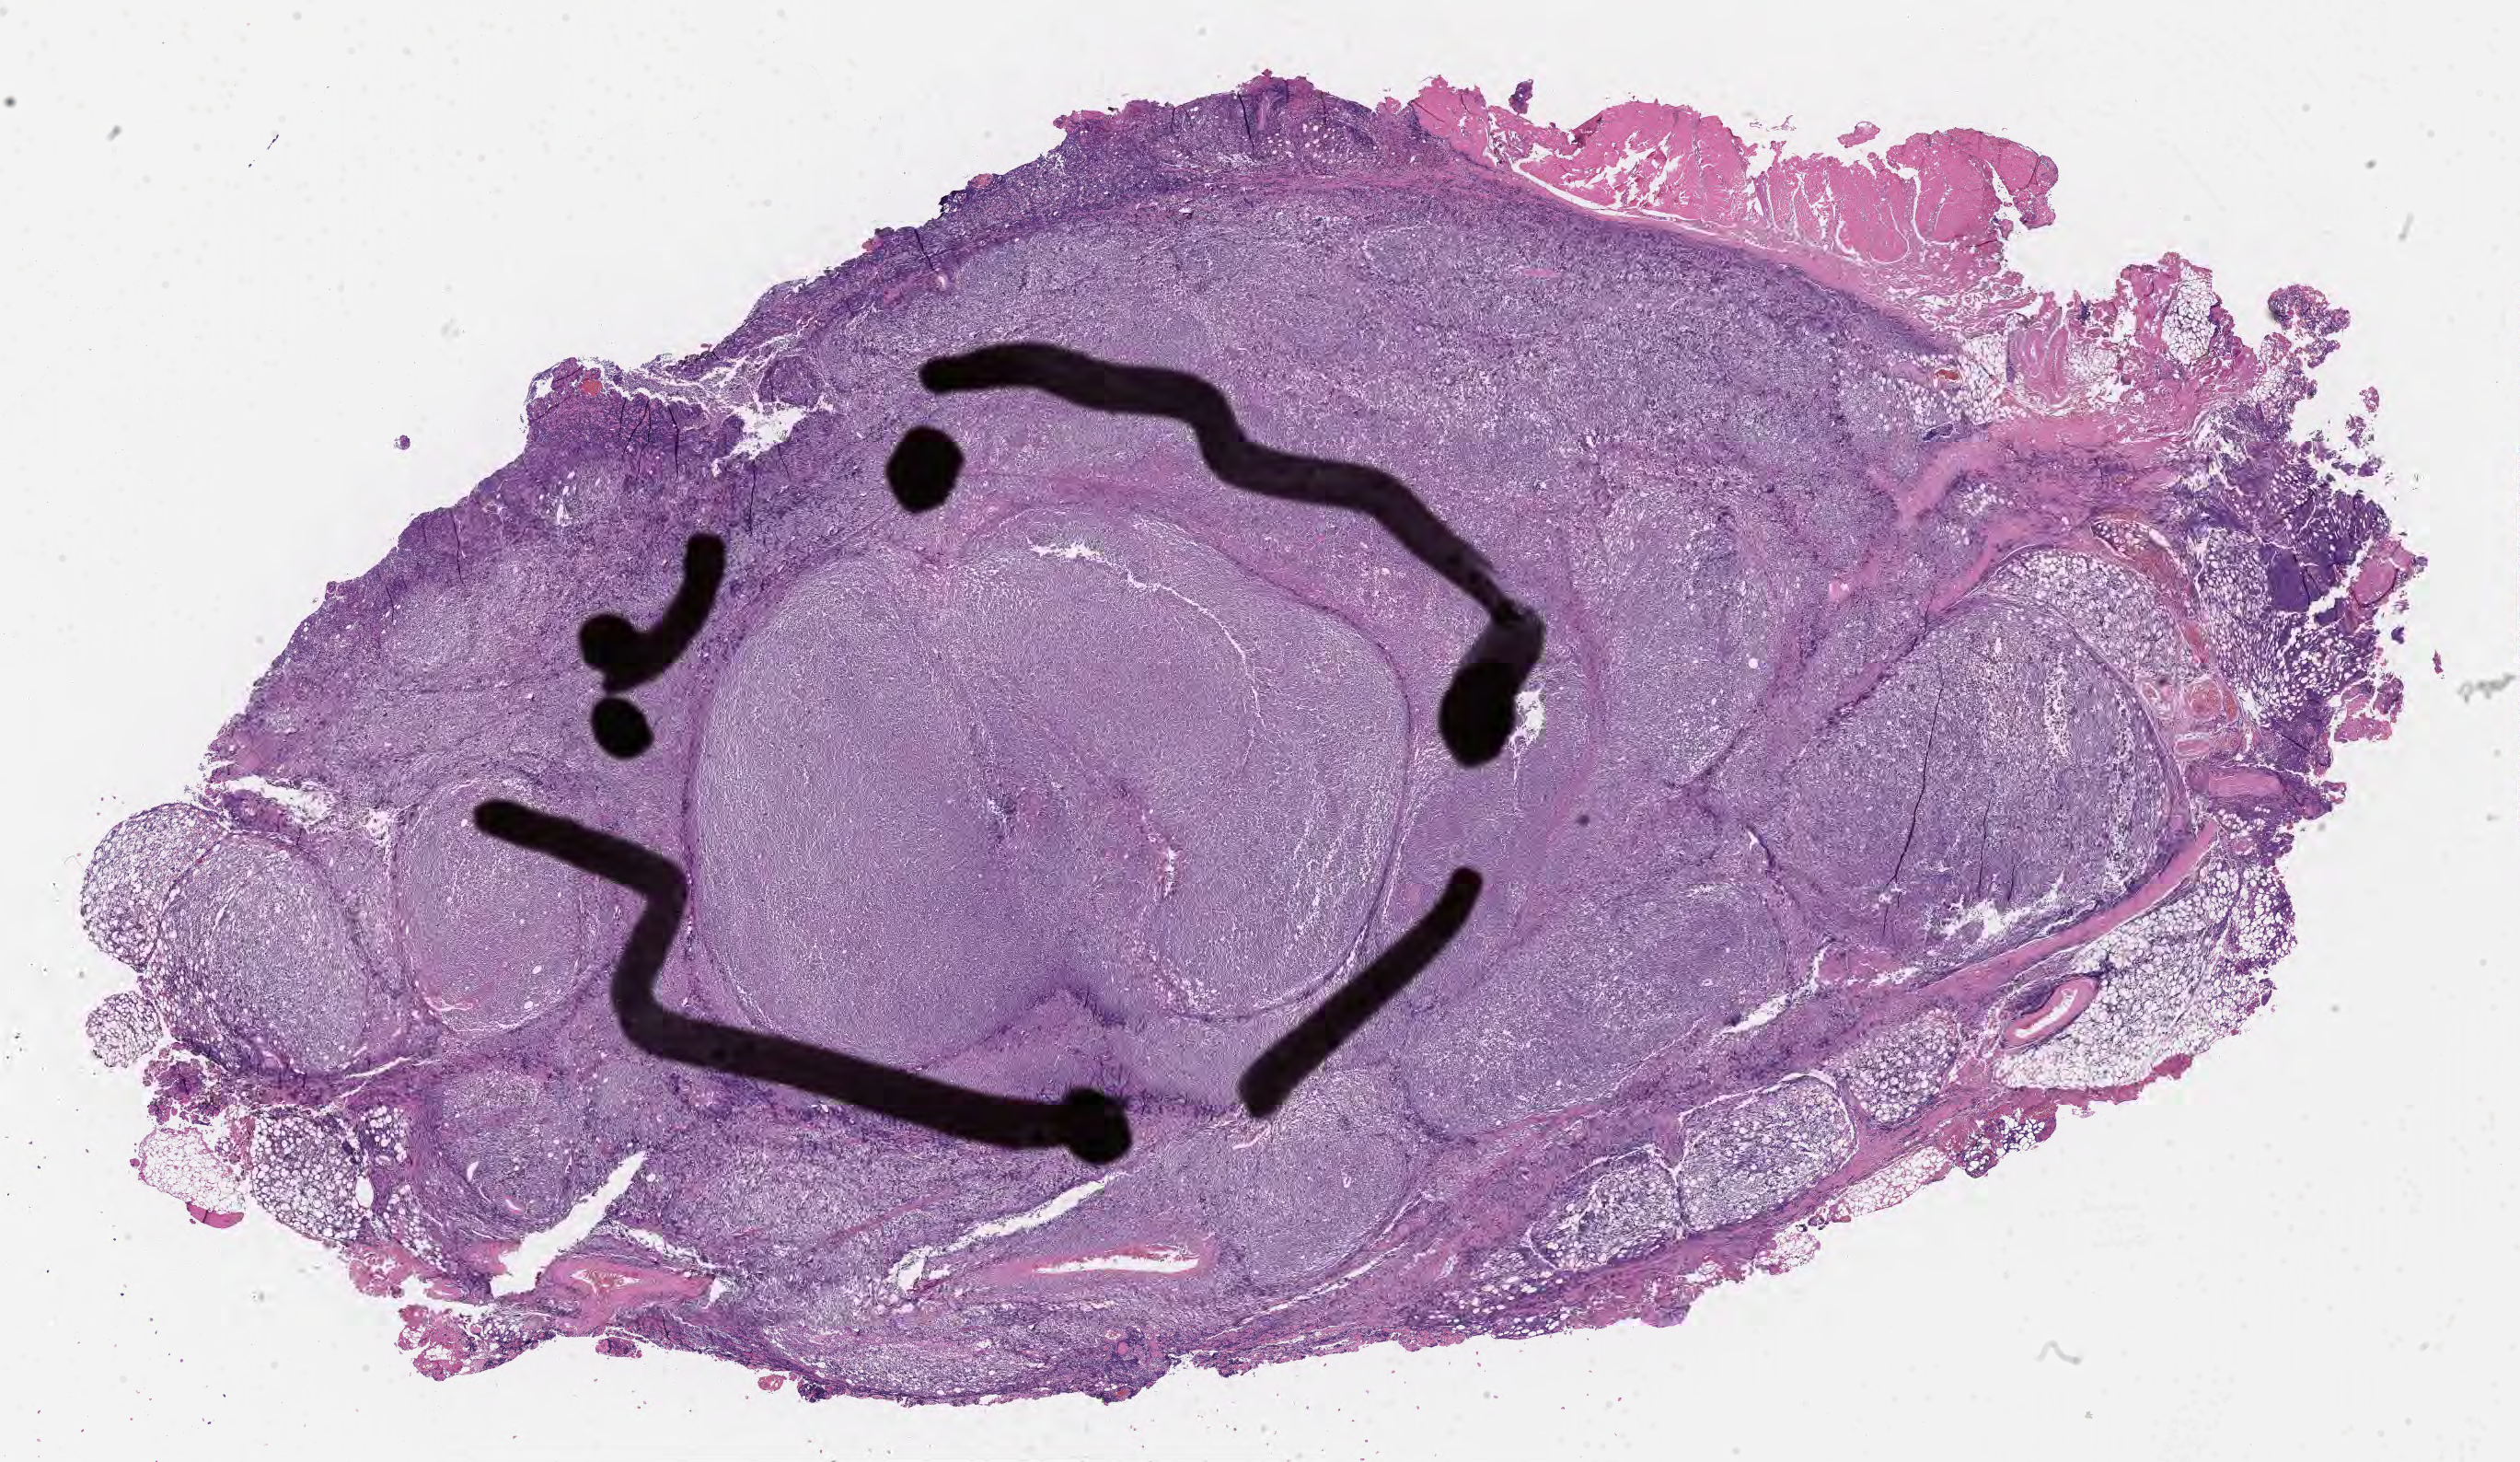
Whole-slide image, hematoxylin and eosin (H&E) stain, shown as a low-resolution overview of the whole scanned area (about 22.1 x 12.8 mm), specimen: tumor tissue. Male patient; age at initial diagnosis 4 years.
Histologic diagnosis: Burkitt lymphoma, NOS.